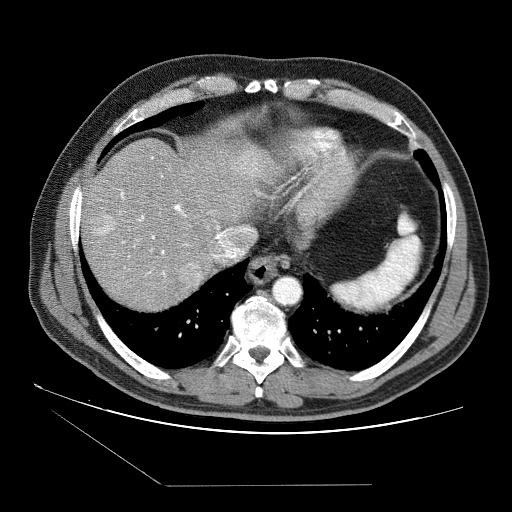
Contrast-enhanced abdominal CT (liver protocol), one axial slice; slice 71 of 87 in the series (ordered by position); 120 kVp; soft-tissue window (W 400 / L 40 HU); 2.5 mm slice thickness; 512 × 512 image matrix. From the clinical record (not read from this slice): diagnosis: hepatocellular carcinoma (patient treated with transarterial chemoembolisation; whether this scan precedes or follows treatment is not stated here); TNM stage (as recorded): Stage-II; Child-Pugh class: B; tumour differentiation: no biopsy; tumour nodularity: multinodular.
Structures marked on this image (semi-automatically segmented with operator editing):
- abdominal aorta: box from (x=273, y=276) to (x=300, y=303) px
- liver parenchyma outside the tumour (the mass and vessels are separate outlines, so this box may not span the whole liver): (x=82, y=138)–(x=276, y=310)
- mass: (x=93, y=215)–(x=201, y=288)
- liver vessels: (x=120, y=157)–(x=258, y=276)